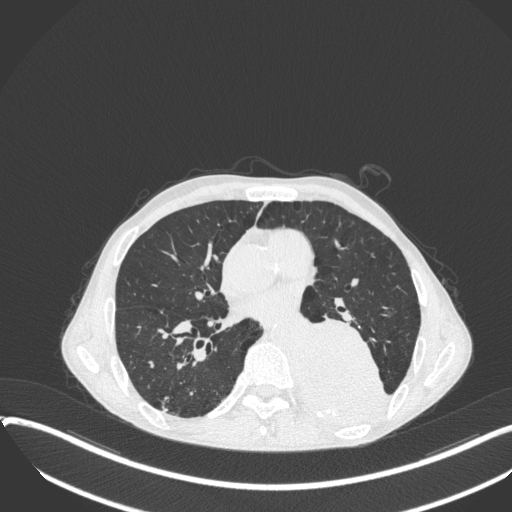
Chest CT, one axial slice. Position 179 of 400 along the scan axis. 120 kVp. Lung window (W 1500 / L -600 HU). 512 × 512 image matrix. Patient: male, 57 years. From the clinical record (not read from this slice): clinical TNM (as recorded): T4 N0 M0.
Annotated regions visible in this slice (rectangle marked by the reading radiologist):
- lung tumour (recorded histology: squamous cell carcinoma): bounding box [x1, y1, x2, y2] px = [301, 319, 391, 421]